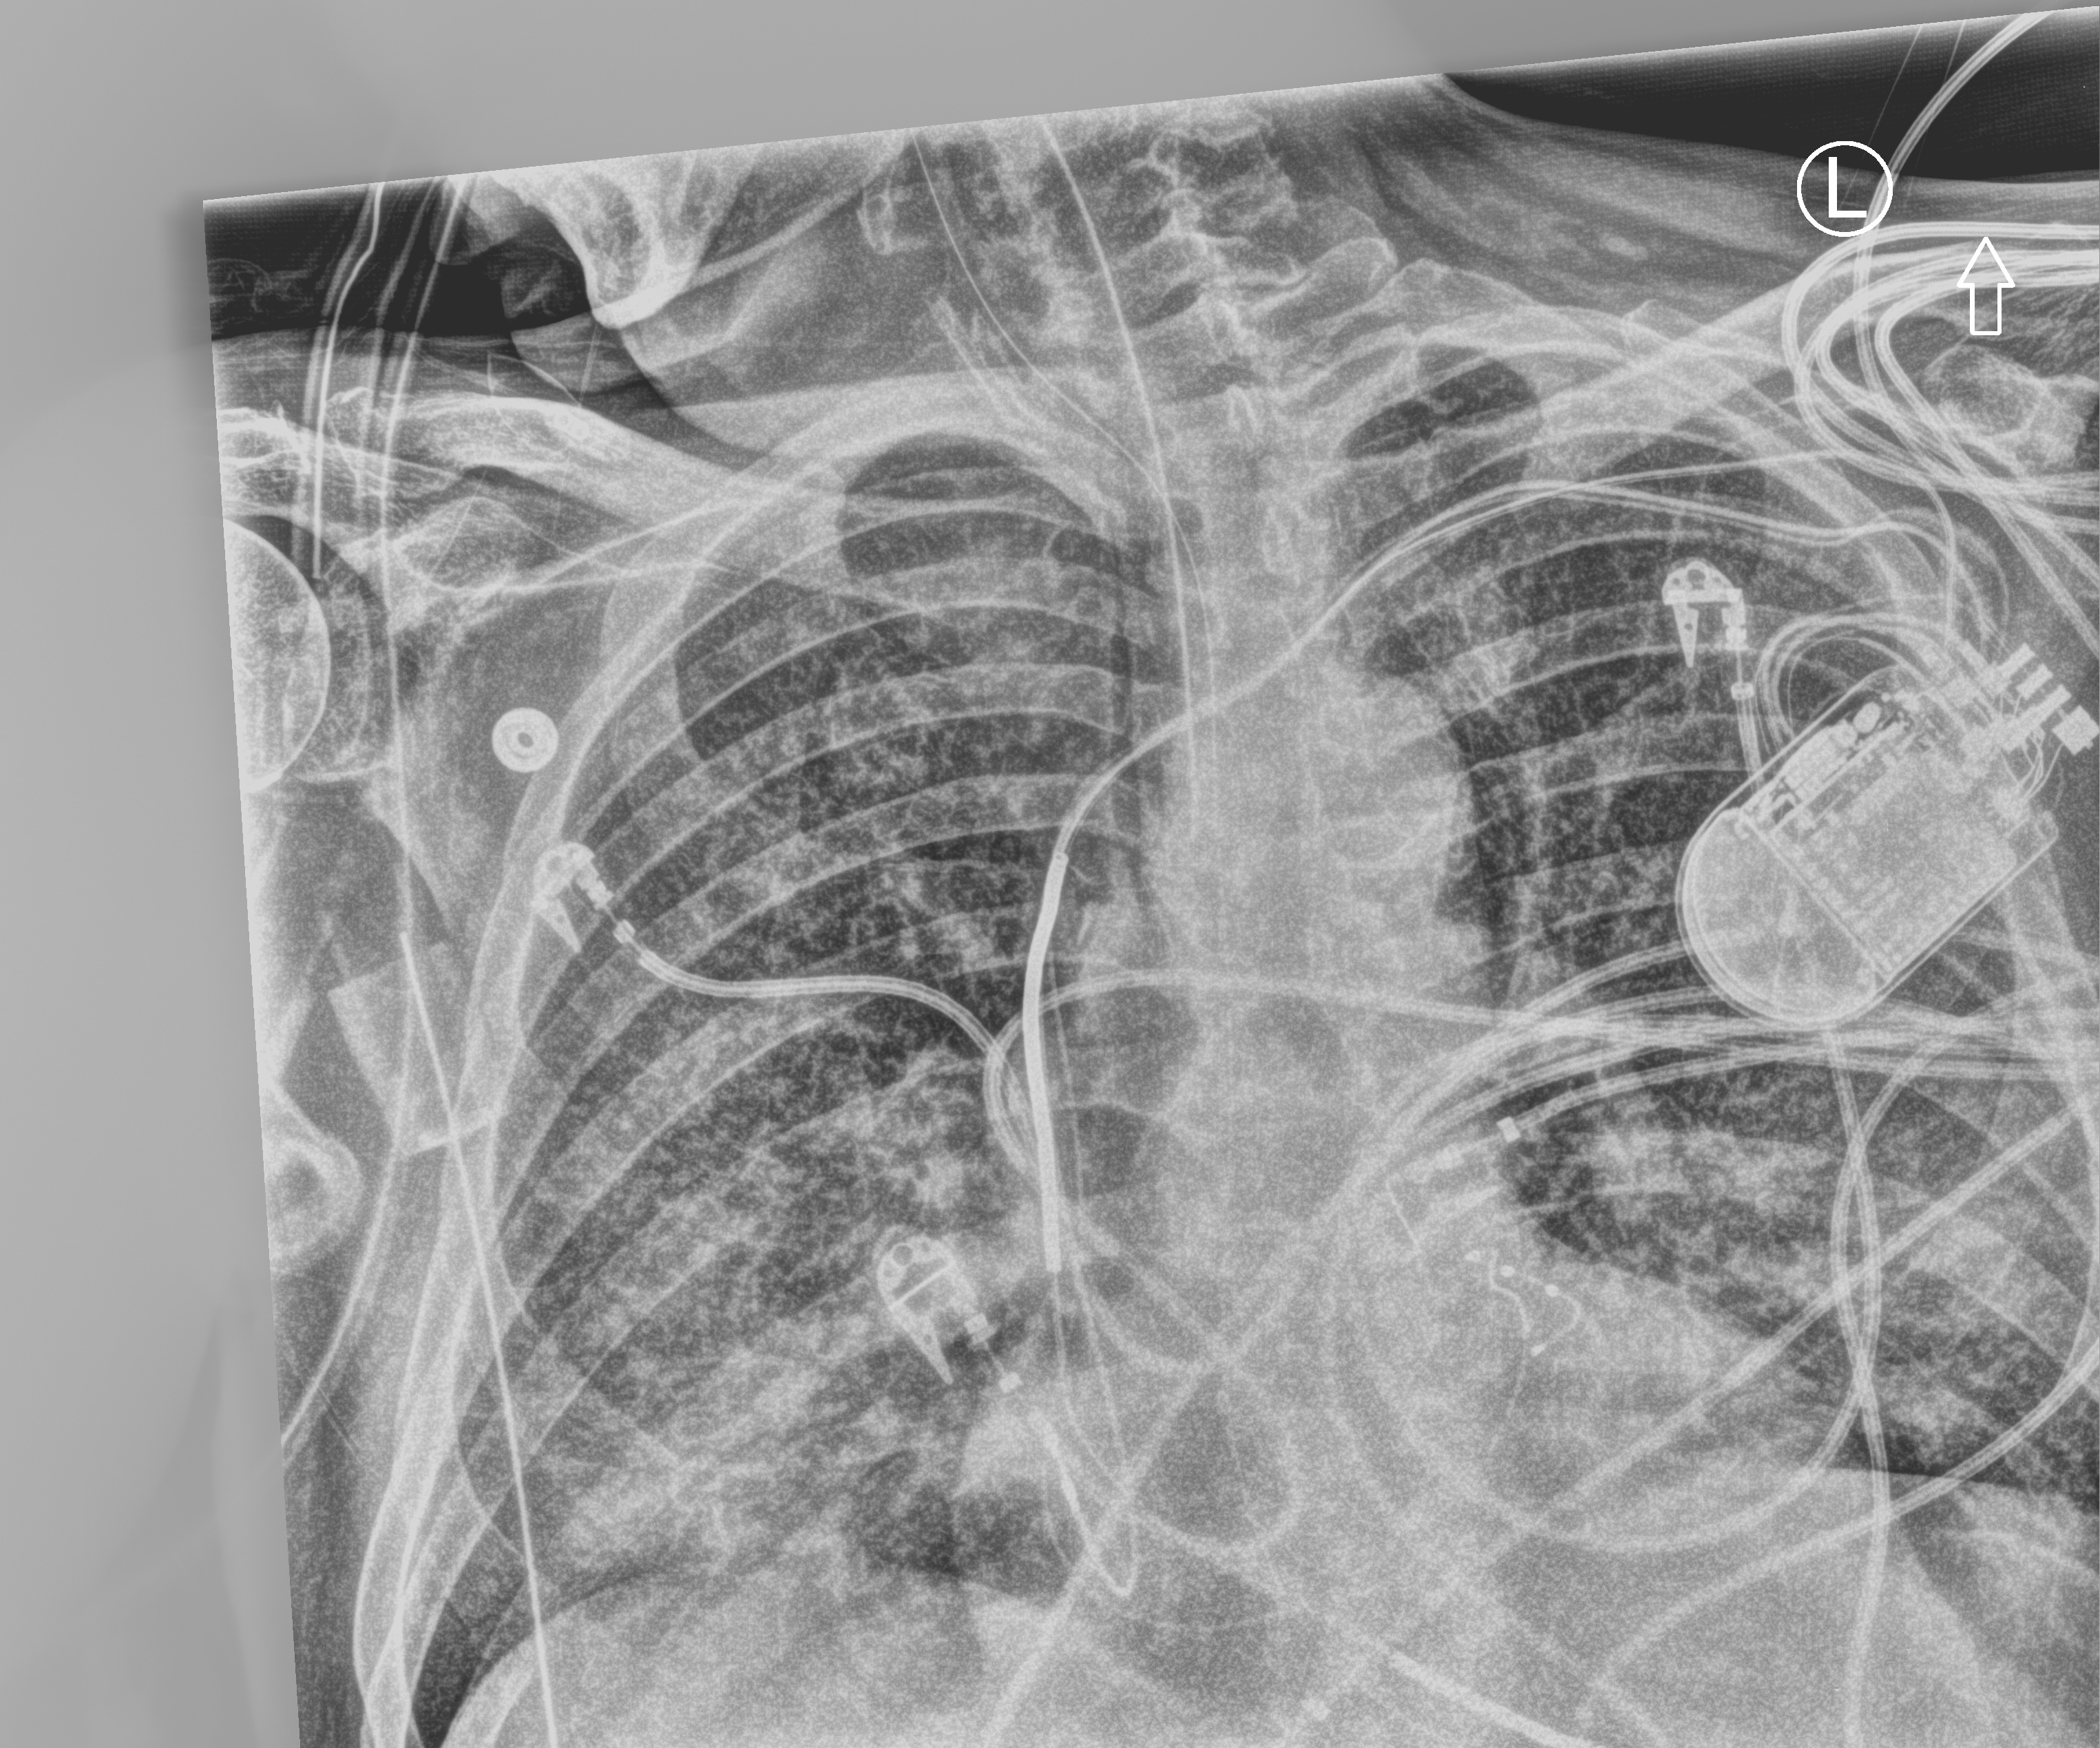
Portable chest radiograph; anteroposterior (AP) projection. Male patient hospitalised with COVID-19, age 60–74 years.
Hospital-stay facts (about this admission, not read from this image; timing relative to this image not recorded):
- admitted to intensive care during this hospital stay: yes
- smoking status (admission record): former
- mechanically ventilated during this hospital stay: yes